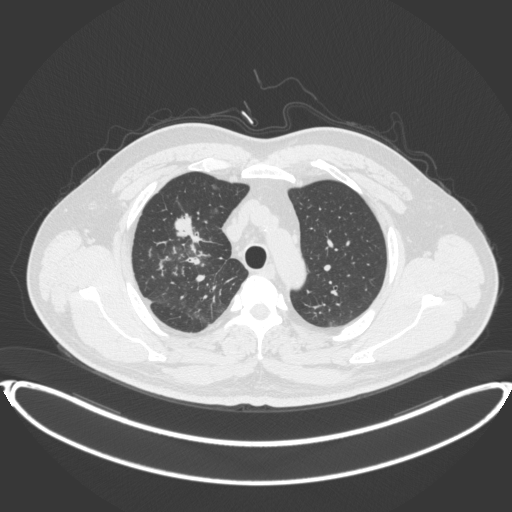
Chest CT, one axial slice. Lung window (W 1500 / L -600 HU). 512 × 512 image matrix, field of view 445 × 445 mm. Male patient, age 53 years. From the clinical record (not read from this slice): clinical TNM (as recorded): T2a N0 M0.
Outlined on this slice (bounding box drawn by a radiologist):
- lung tumour (recorded histology: adenocarcinoma): bounding box [x1, y1, x2, y2] px = [175, 211, 206, 247]